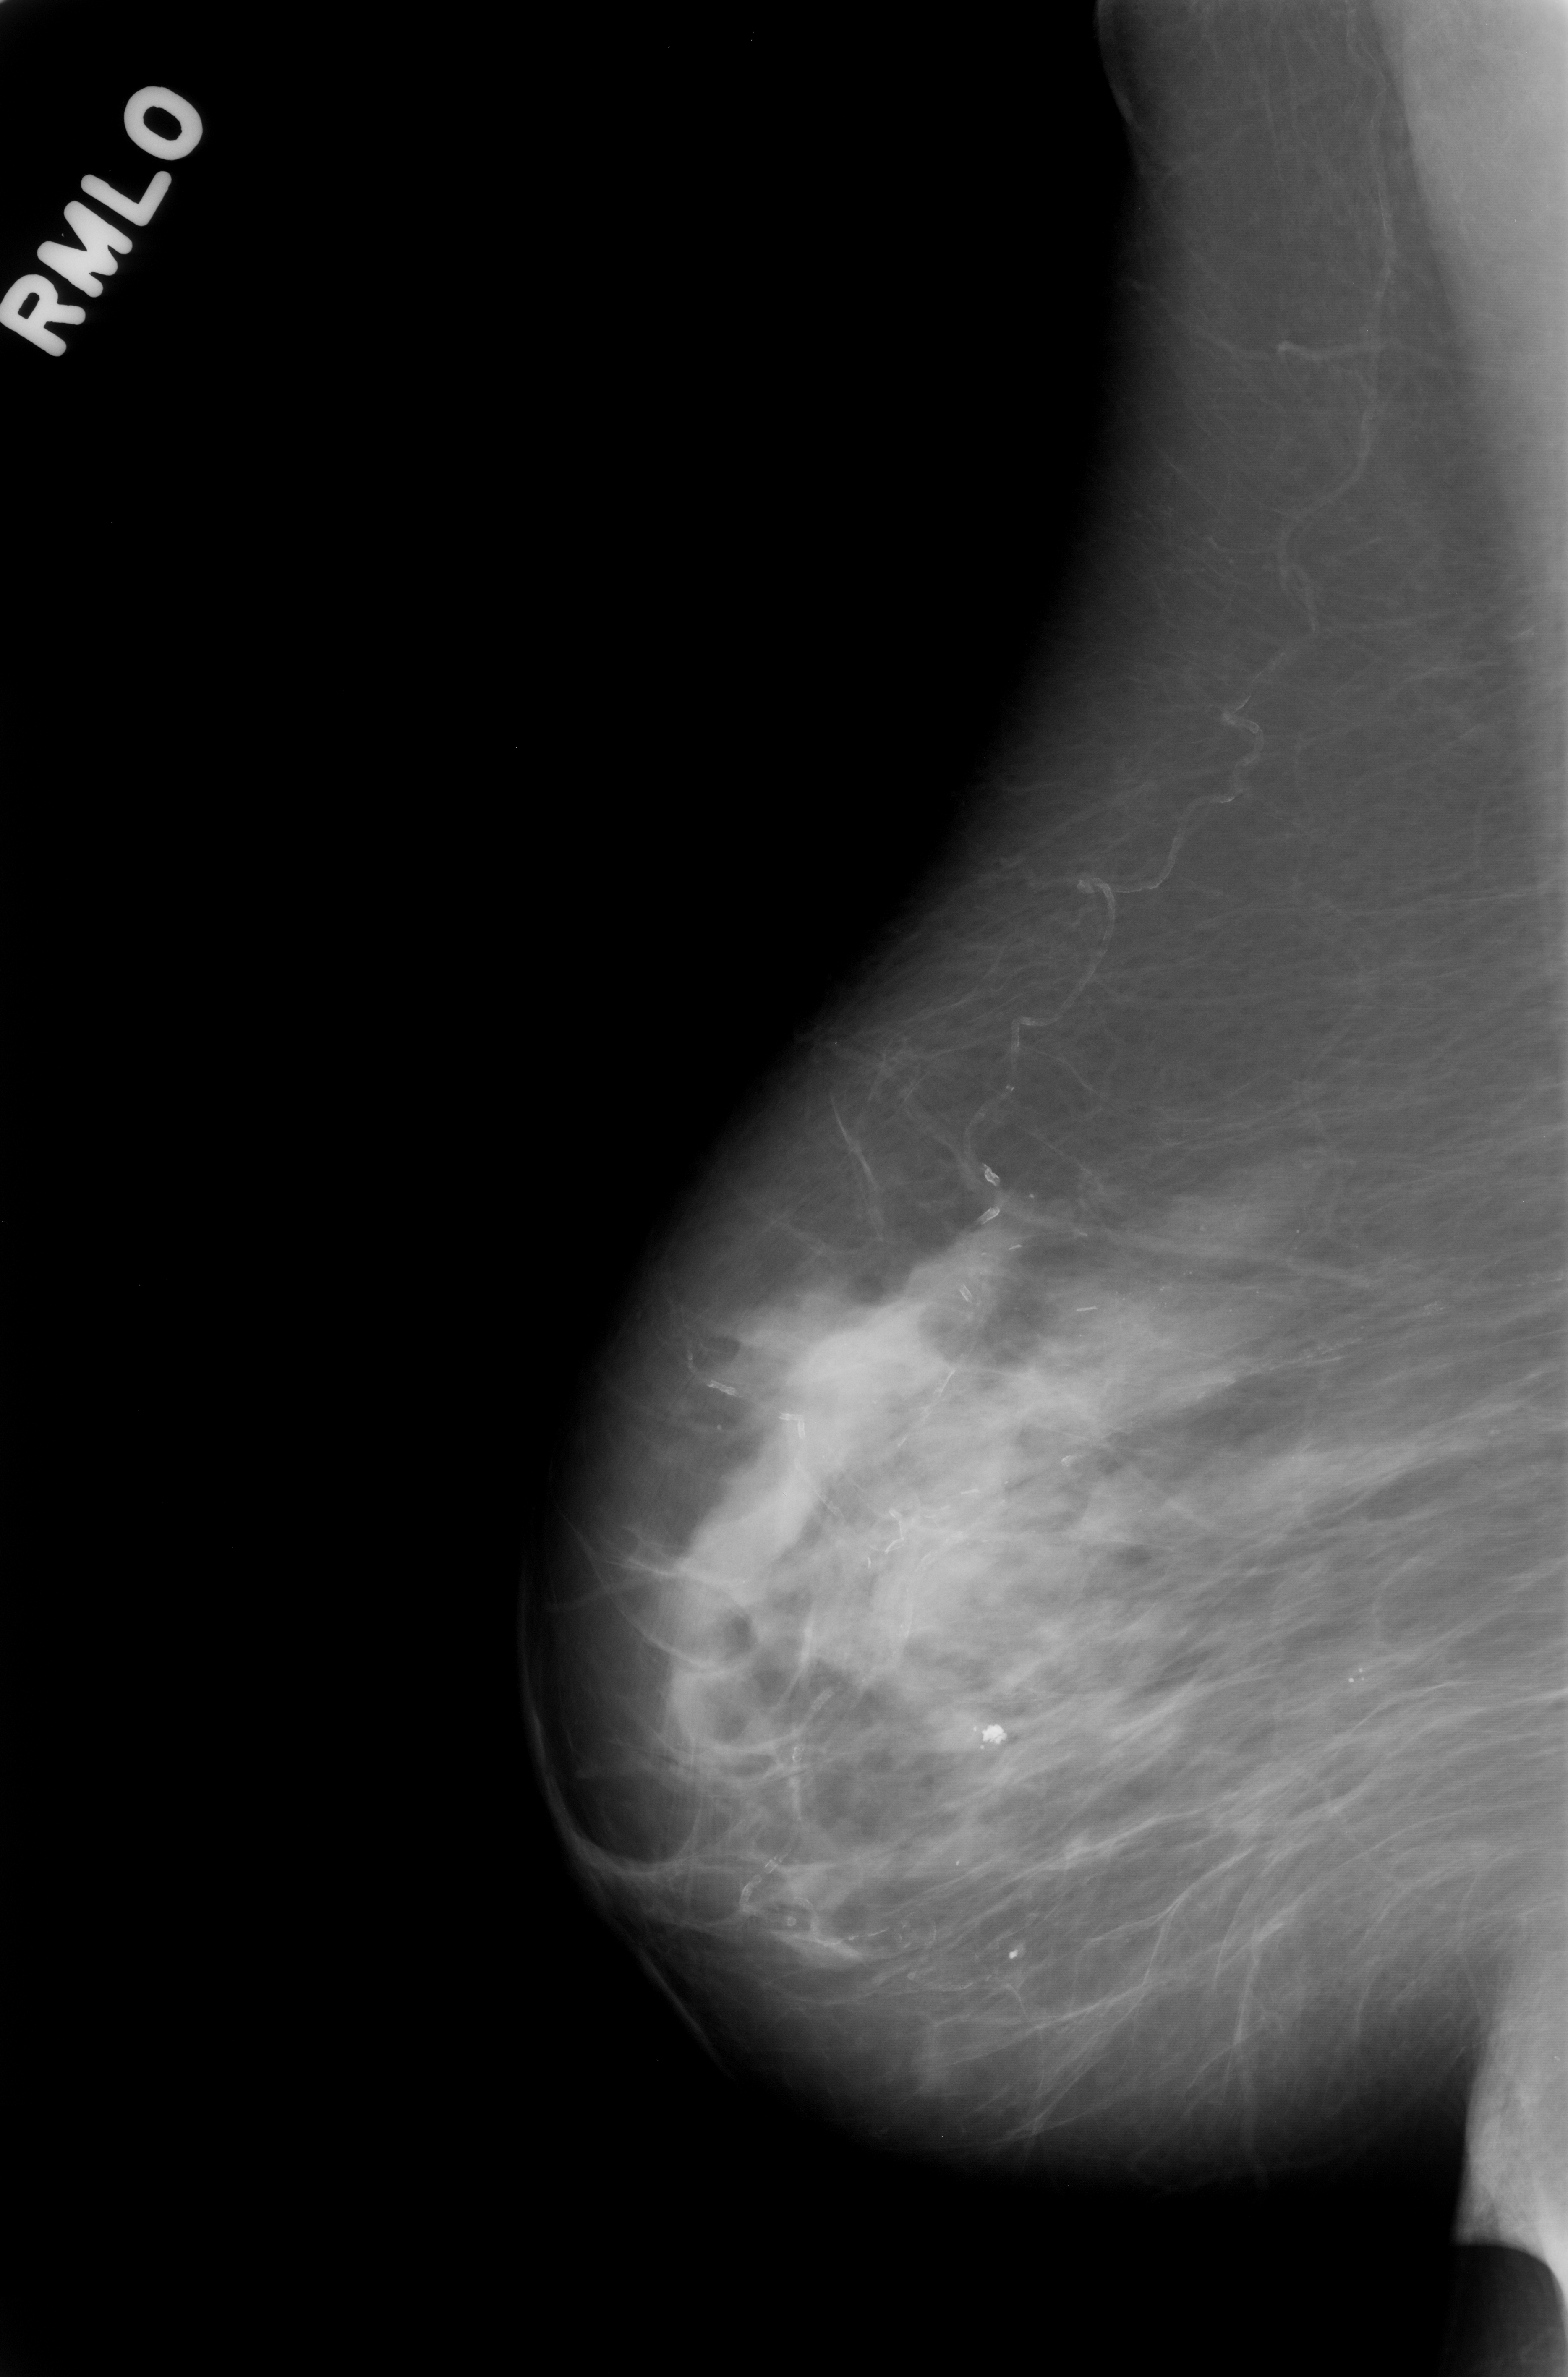
Scanned film-screen mammogram; right breast; mediolateral oblique (MLO) view; 1568 × 2377 image matrix.
Expert-marked regions of interest on this film, with their recorded descriptors:
- calcifications, morphology punctate, distribution segmental; BI-RADS assessment category 4; subtlety rating 2 on a 1 (subtle) to 5 (obvious) scale; pathology result (as recorded, not read from the image): benign: bounding box [x1, y1, x2, y2] px = [977, 1161, 1324, 1508]